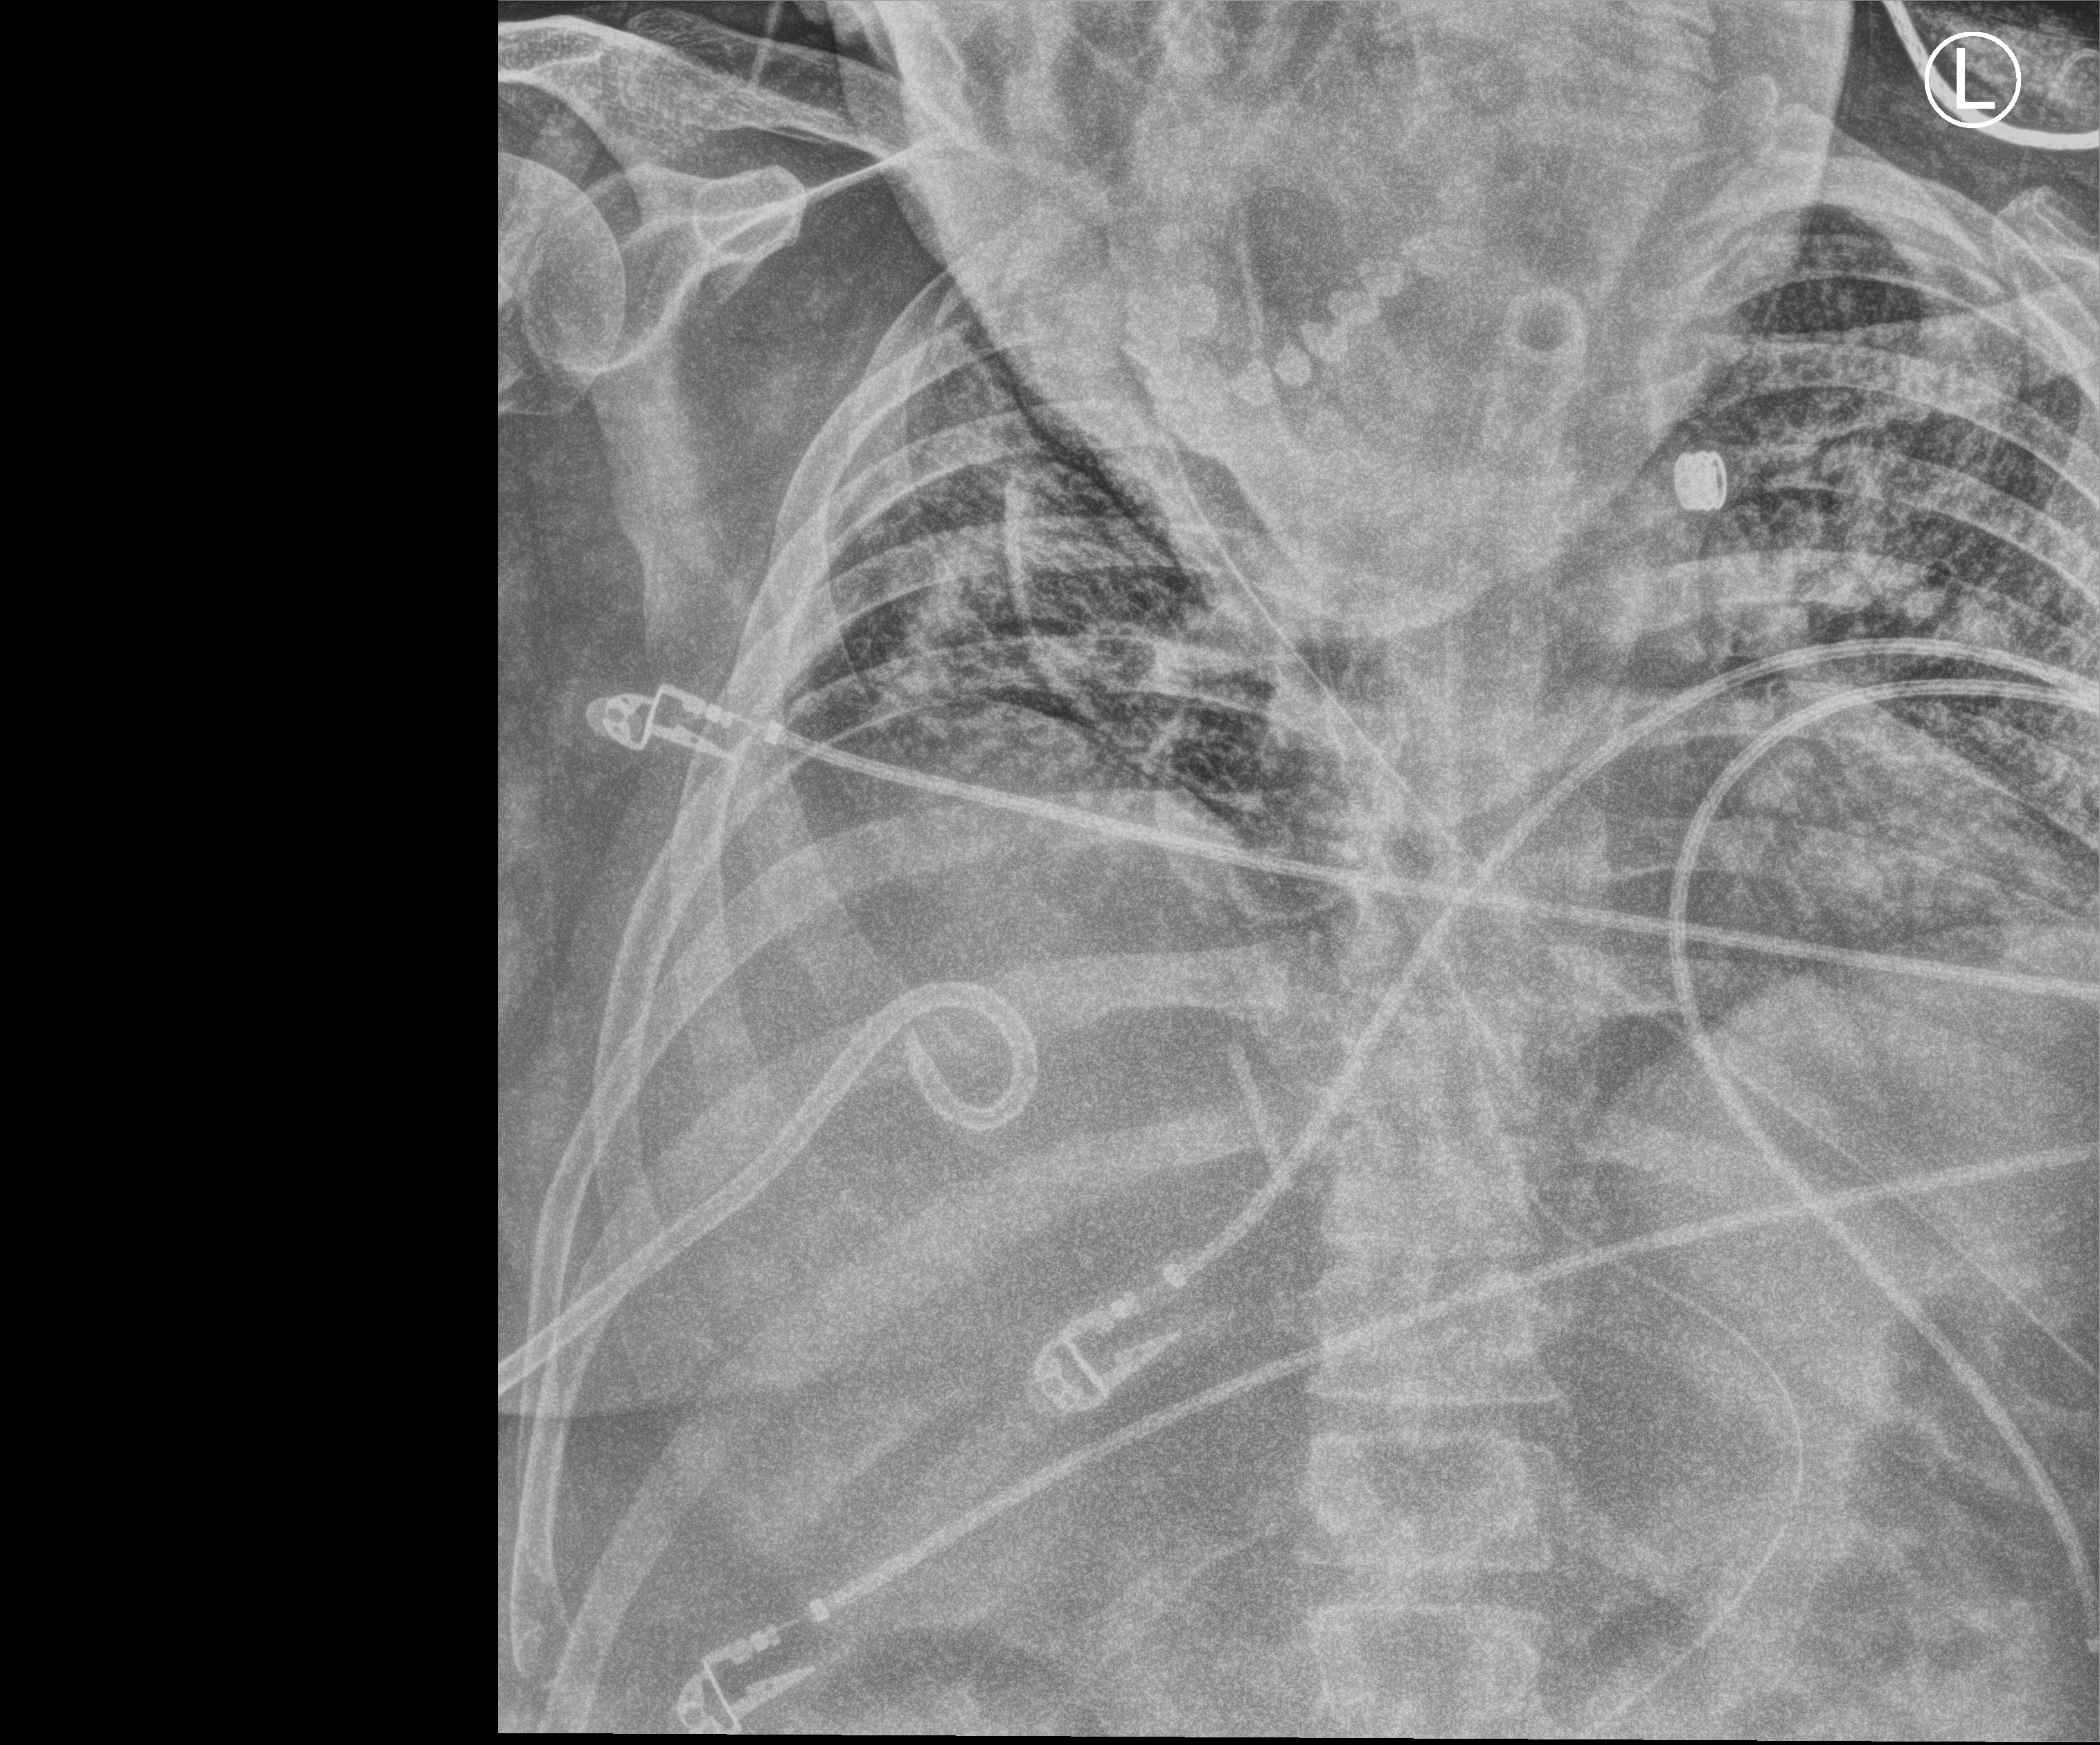
Portable chest radiograph. Male patient hospitalised with COVID-19, age 18–59 years.
Hospital-stay facts (about this admission, not read from this image; timing relative to this image not recorded): admitted to intensive care during this hospital stay: yes; COPD (admission record): no.